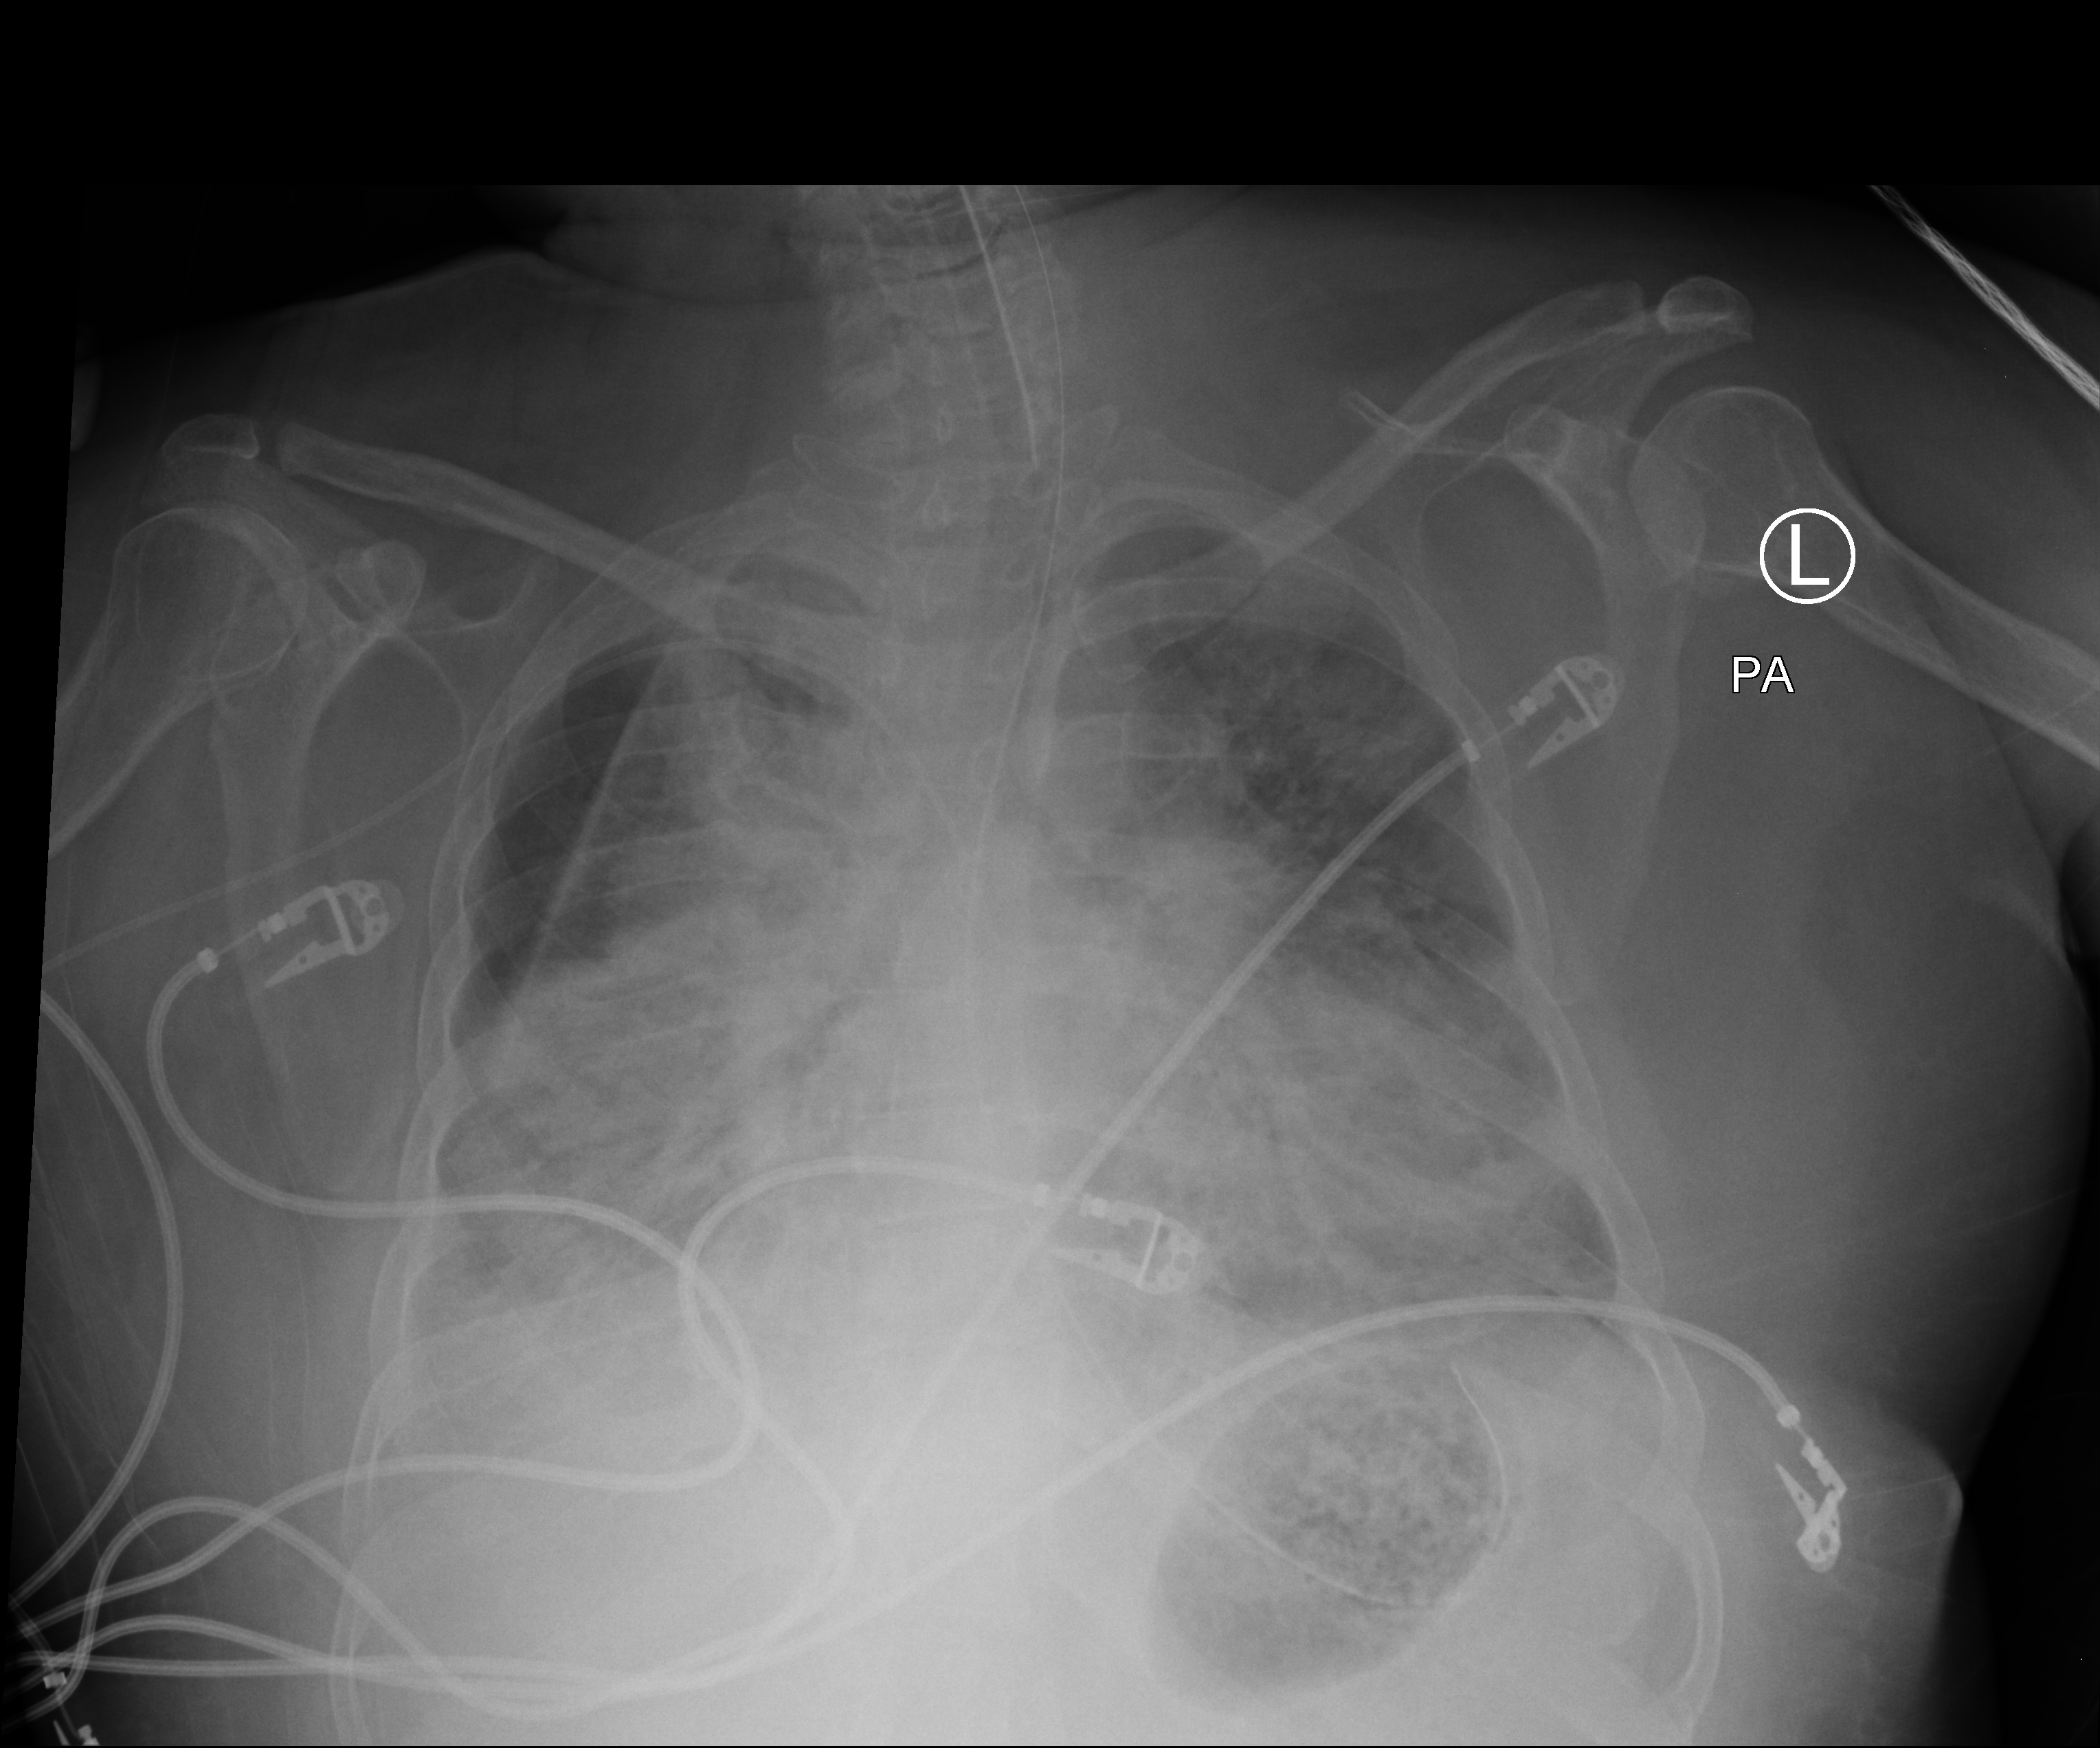
Bedside chest radiograph (computed radiography). Adult patient hospitalised with COVID-19, age 18–59 years.
Admission-level facts for this patient (not findings on this image; timing relative to this image not recorded):
- mechanically ventilated during this hospital stay: yes